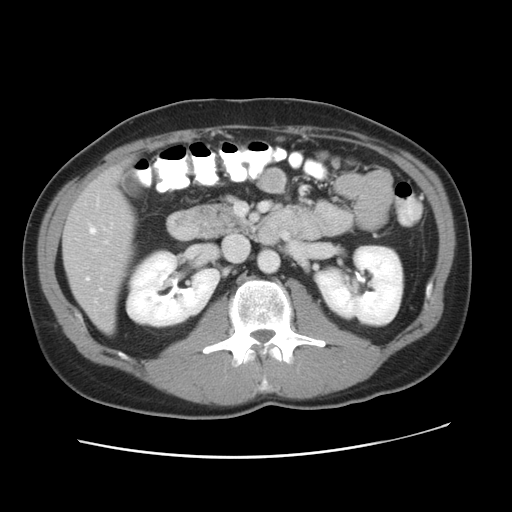
Contrast-enhanced abdominal CT, one axial slice; slice 21 of 49 in the series (ordered by position); reconstruction kernel STANDARD; 120 kVp; intravenous contrast given; soft-tissue window (W 400 / L 40 HU); 5 mm slice thickness; 512 × 512 image matrix, field of view 363 × 363 mm. Male patient, age 41 years. From the clinical record (not read from this slice): diagnosis: colorectal cancer liver metastases, imaged before liver resection; multiple liver metastases: yes; largest metastasis: 0.7 cm; disease in both lobes: yes.
Annotated regions visible in this slice (manually delineated by an expert):
- hepatic veins: bounding box <86,226,101,301> (left, top, right, bottom; pixels)
- liver: <64,166,134,331>
- portal vein (with intrahepatic branches): <105,240,108,243>